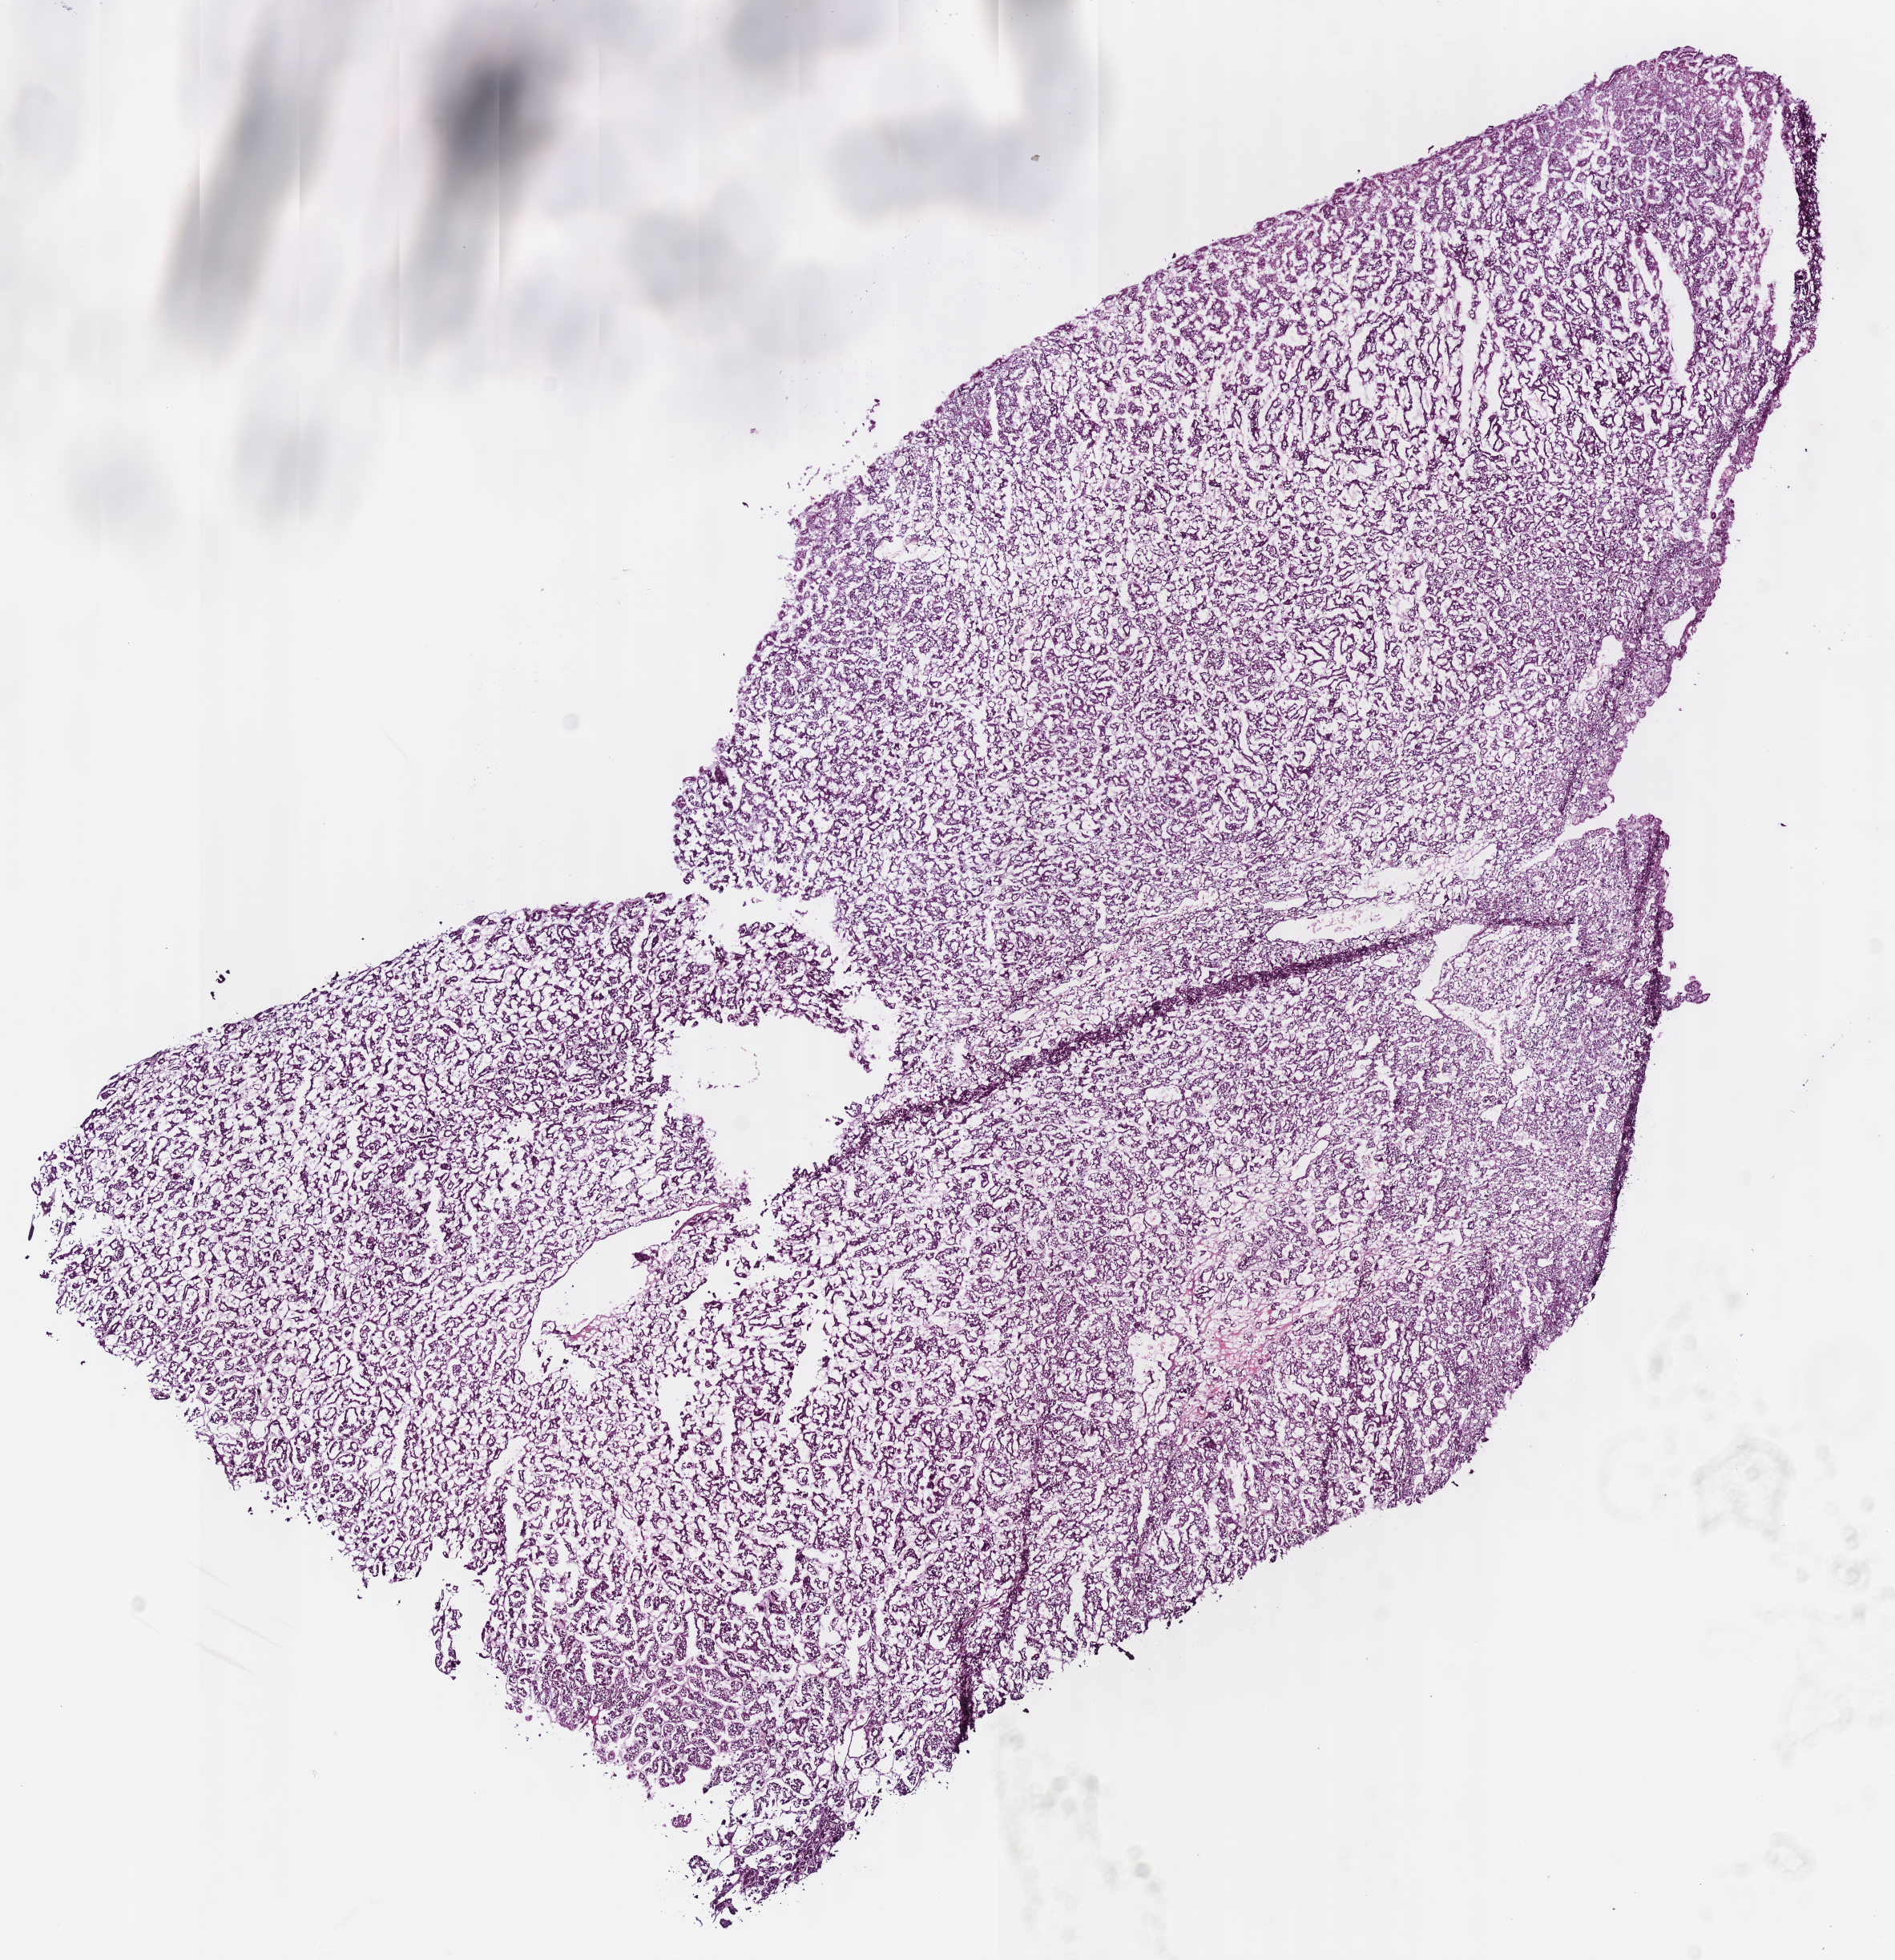
Whole-slide histology image, H&E — a low-resolution overview of the entire scanned area, about 9.3 x 9.6 mm; frozen section; kidney, primary tumour sample. Male, age 67 years at initial diagnosis.
Diagnosis: Renal cell carcinoma, chromophobe type.